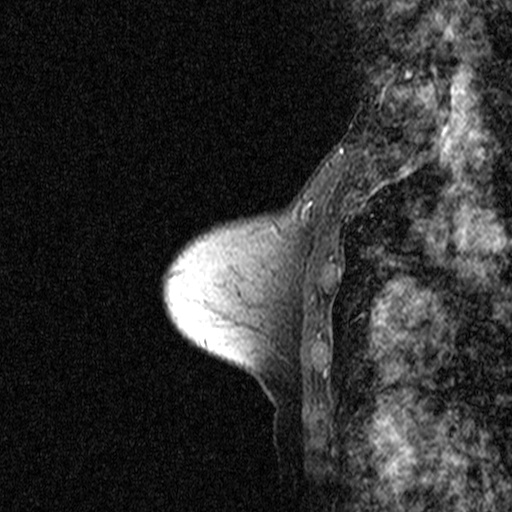
Breast MRI (dynamic contrast-enhanced), one sagittal slice. Position 14 of 44 along the scan axis. Dynamic contrast-enhanced study with each time point stored as its own series, time point 2 of 3 at this slice position (early post-contrast, ordered by acquisition time). 1.5 T. TE 4.5 ms, TR 11 ms. 2.27 mm slice thickness. 512 × 512 image matrix, field of view 200 × 200 mm. Patient: female, 53 years. Case-level facts recorded for this patient, not image findings: setting: breast cancer imaged before/during neoadjuvant chemotherapy; receptor status: HR-positive, HER2-negative.
Structures marked on this image (semi-automatically segmented with operator editing):
- analysis volume of interest (the breast-tissue region the enhancement analysis was run in; not a lesion): bounding box (x1, y1, x2, y2) in pixels: (200, 178, 317, 309)
- tumour enhancement mask (voxels above the 90 % enhancement threshold inside the analysis volume of interest): (306, 202, 312, 220)